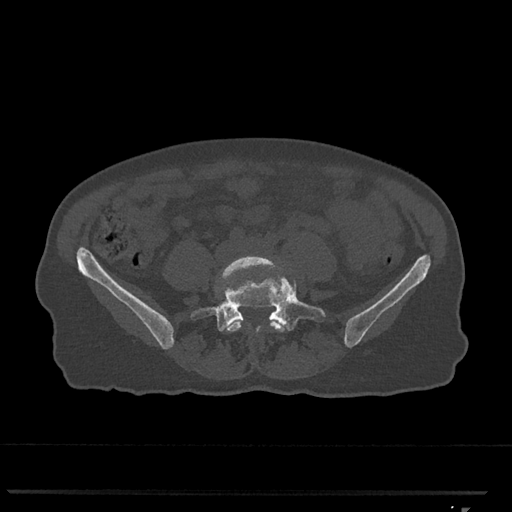
CT including the spine, one axial slice. Slice 170 of 793 in the series (ordered by position). Reconstruction kernel Br40s/3. 120 kVp. Bone window (W 1800 / L 400 HU). 512 × 512 image matrix. Female patient, age 62 years. From the clinical record (not read from this slice): primary cancer: renal.
Annotated regions visible in this slice (semi-automatic segmentation, software-assisted and operator-edited):
- L4 vertebra: box from (x=217, y=255) to (x=285, y=333) px
- L5 vertebra: (x=190, y=261)–(x=326, y=332)